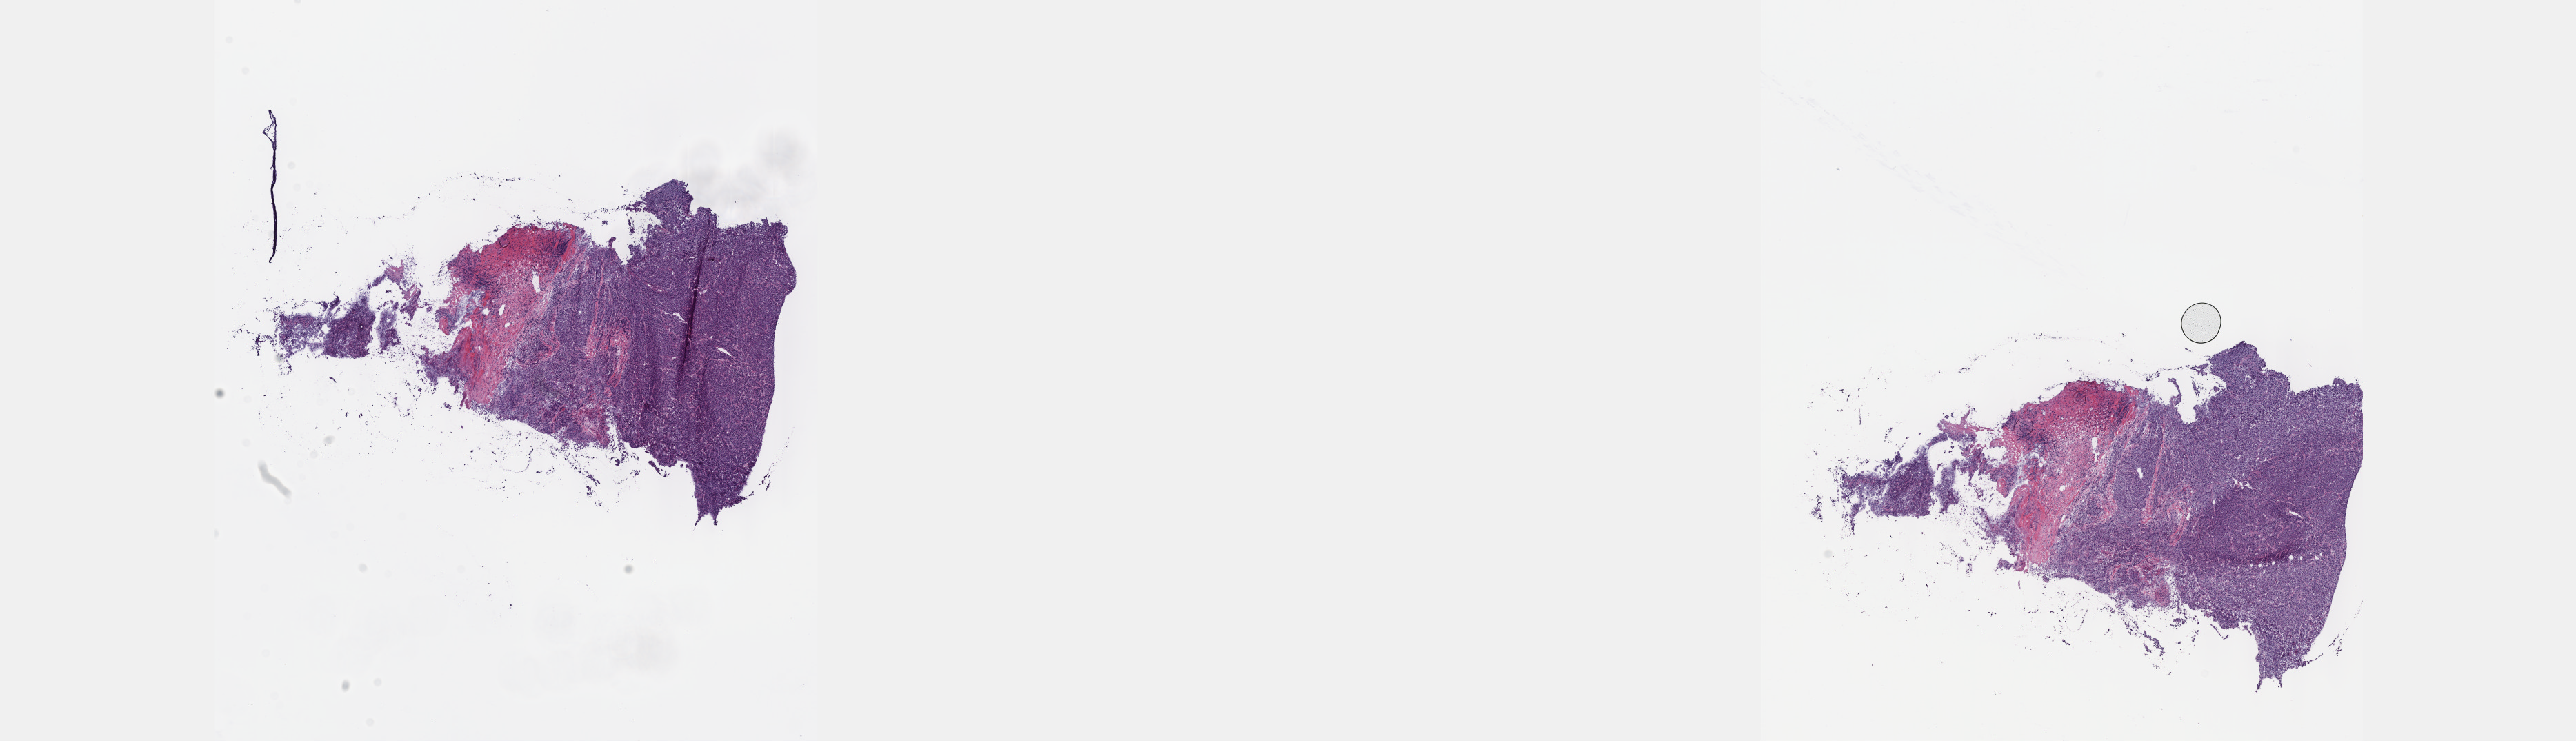
Whole-slide histology image, H&E-stained, a low-resolution overview of the entire scanned area, about 30.2 x 8.7 mm; frozen section from the top of the tissue portion; liver, primary tumour sample. Male patient; age at initial diagnosis 72 years. Histologic grade: G1 (well differentiated). Composition of this section per pathologist review: tumour cells 80%, tumour nuclei 85%, normal cells 0%, stromal cells 20%, necrosis 0%. Infiltration values recorded for this section: lymphocyte infiltration 0%, monocyte infiltration 0%, neutrophil infiltration 0%.
Diagnosis: Hepatocellular carcinoma, NOS.